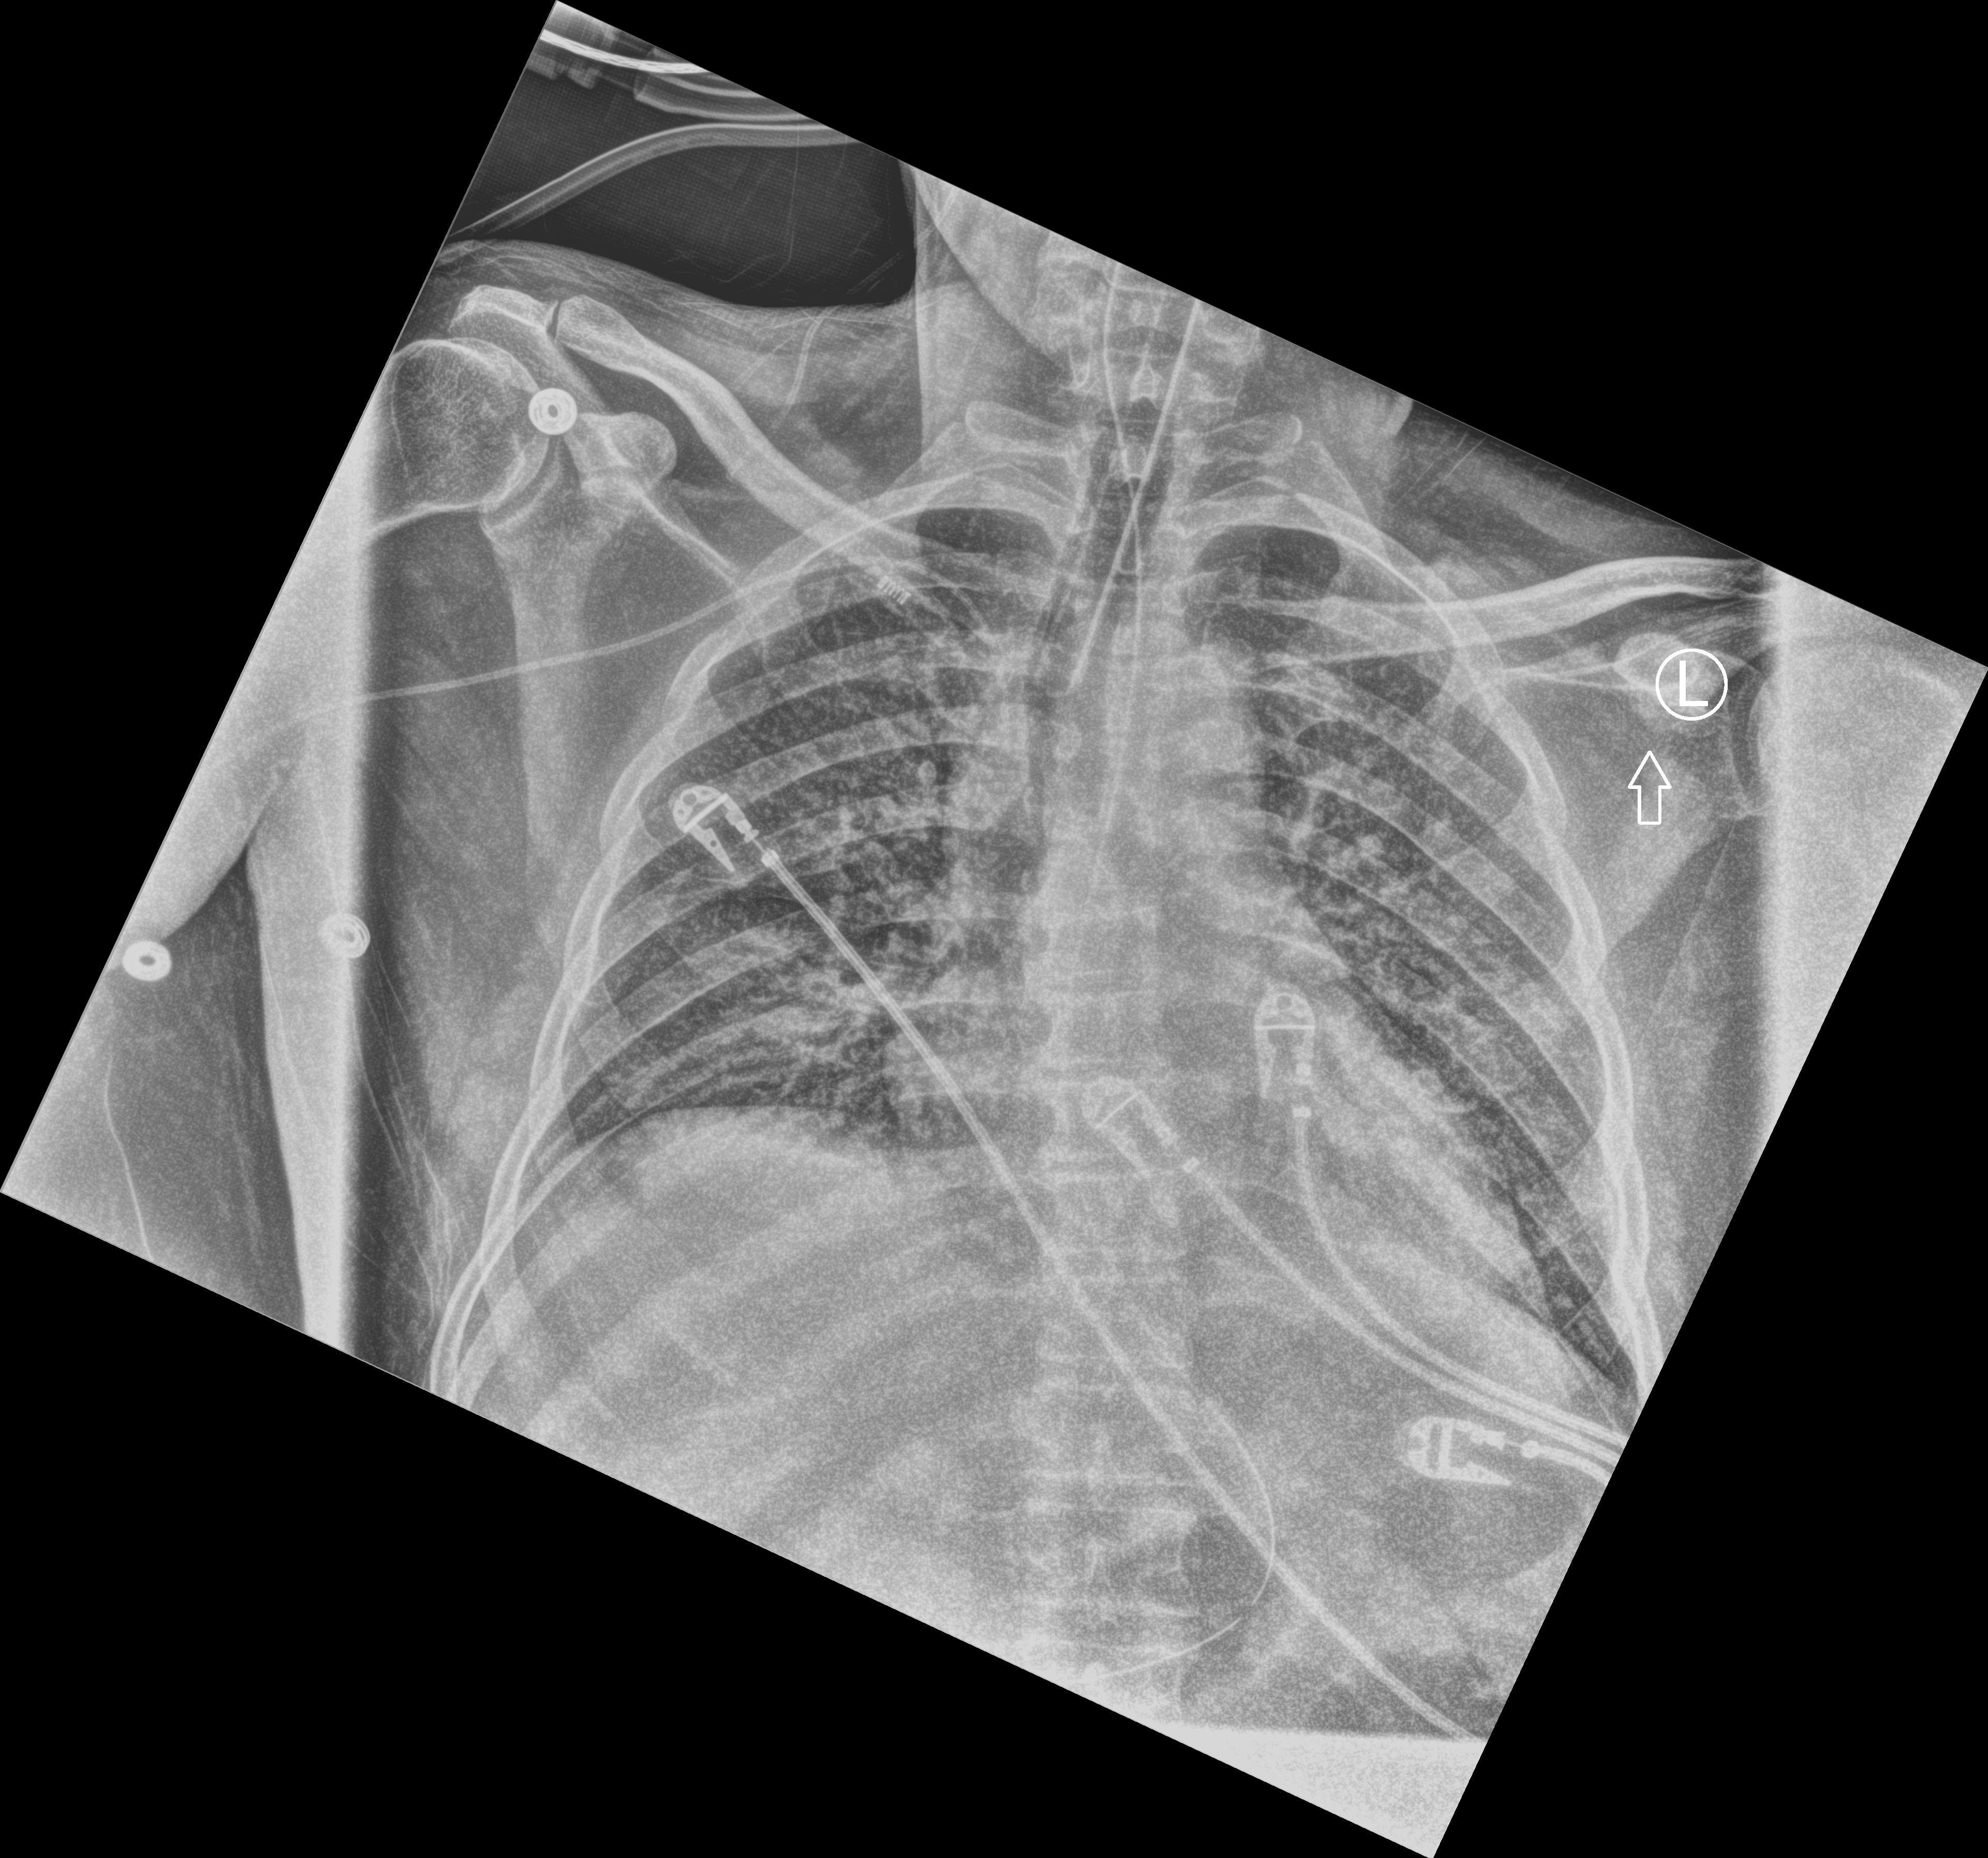
Portable chest radiograph, anteroposterior (AP) projection. Patient hospitalised with COVID-19; male, aged 18–59 years.
Hospital-stay facts (about this admission, not read from this image; timing relative to this image not recorded): COPD (admission record): no; admitted to intensive care during this hospital stay: yes.